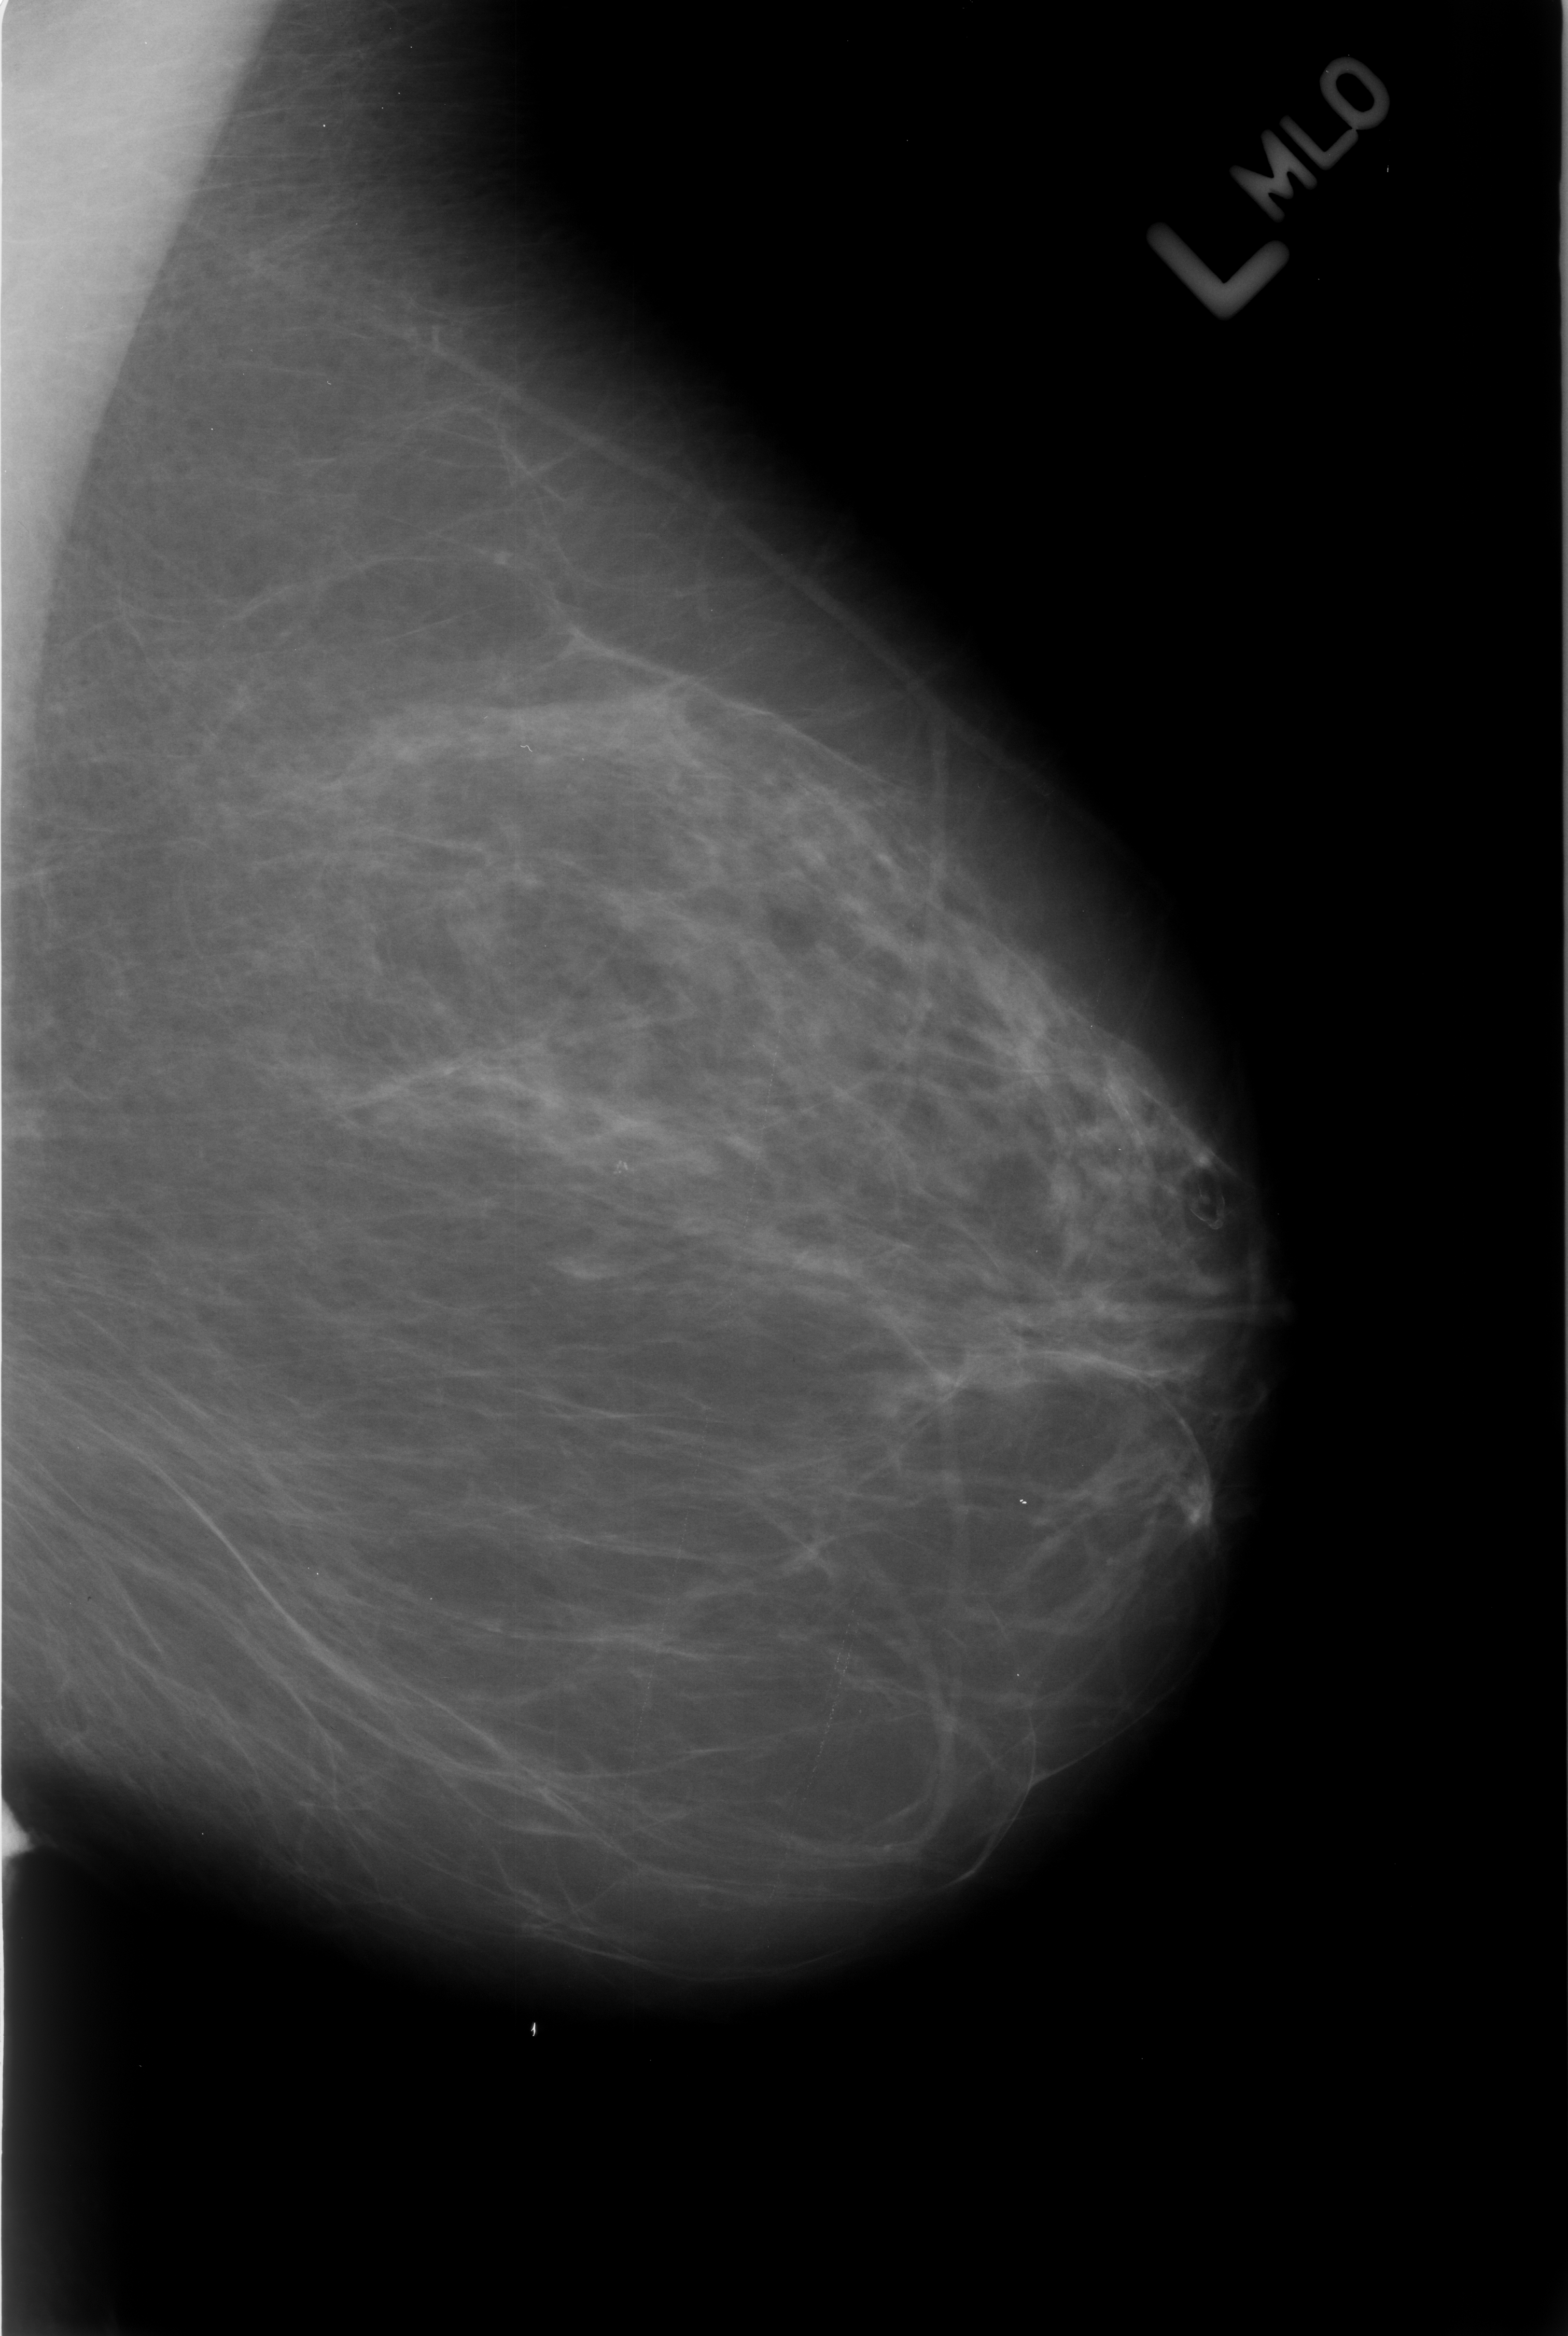
Digitized screen-film mammogram. Left breast. Mediolateral oblique (MLO) view. BI-RADS breast density category 2 (scale 1–4). 1568 × 2336 image matrix.
Expert-marked regions of interest on this film, with their recorded descriptors:
- calcifications, morphology punctate / pleomorphic, distribution clustered; BI-RADS assessment category 4; subtlety rating 3 on a 1 (subtle) to 5 (obvious) scale; pathology (as recorded): benign: box from (x=572, y=1132) to (x=656, y=1208) px